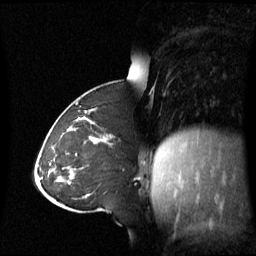
Breast MRI (dynamic contrast-enhanced), one sagittal slice; slice 27 of 60 in the series (ordered by position); dynamic contrast-enhanced series, image 2 of 3 at this slice position (ordered by acquisition); 1.5 T; TE 4.2 ms, TR 8.4 ms; 2.8 mm slice thickness; 256 × 256 image matrix, field of view 270 × 270 mm. Female patient, age 43 years. Case-level facts recorded for this patient, not image findings: setting: breast cancer imaged before/during neoadjuvant chemotherapy; receptor status: triple-negative.
Outlined on this slice (semi-automatically segmented with operator editing):
- analysis volume of interest (the breast-tissue region the enhancement analysis was run in; not a lesion): bounding box (x1, y1, x2, y2) in pixels: (55, 124, 112, 173)
- tumour enhancement mask (voxels above the 70 % enhancement threshold inside the analysis volume of interest): (89, 137, 98, 143)